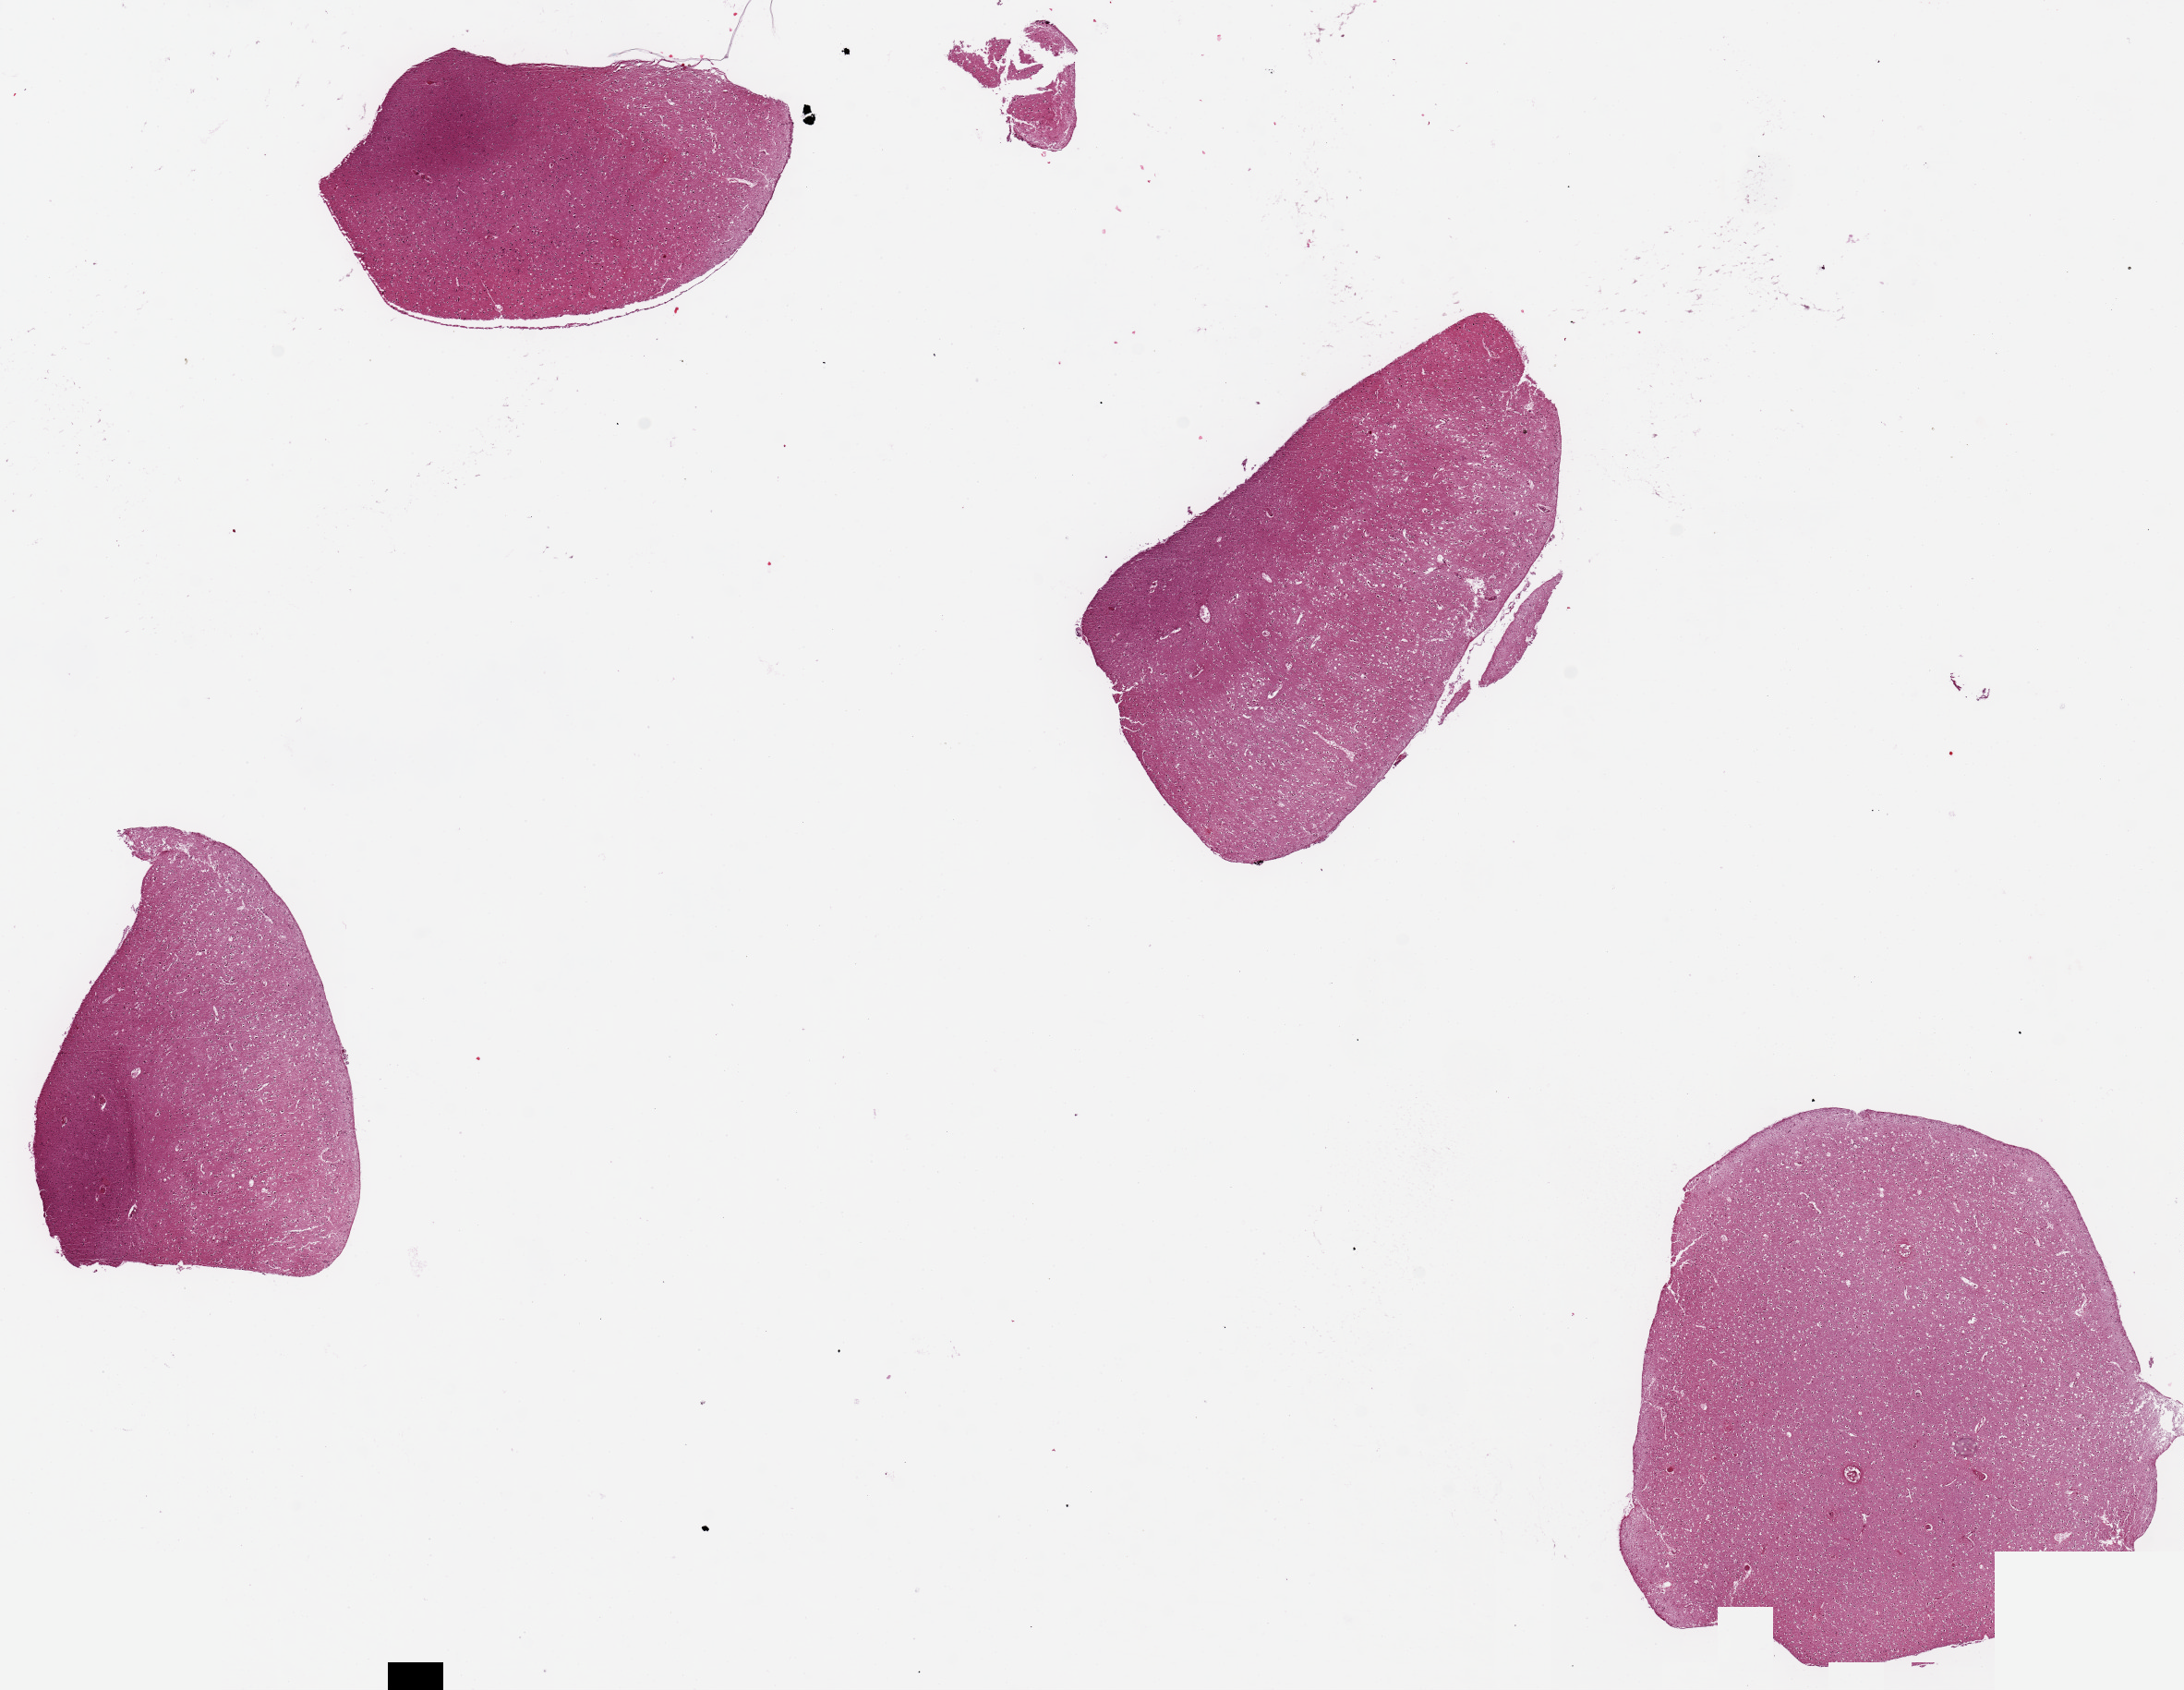
Whole-slide image, haematoxylin and eosin stain — shown as a low-resolution overview of the whole scanned area (about 18.7 x 14.5 mm), PAXgene-fixed paraffin-embedded (PFPE) section, target tissue: cerebral cortex, tissue donor sample. Donor: male.
Review note (as recorded): 4 pieces, up to 5x5mm.